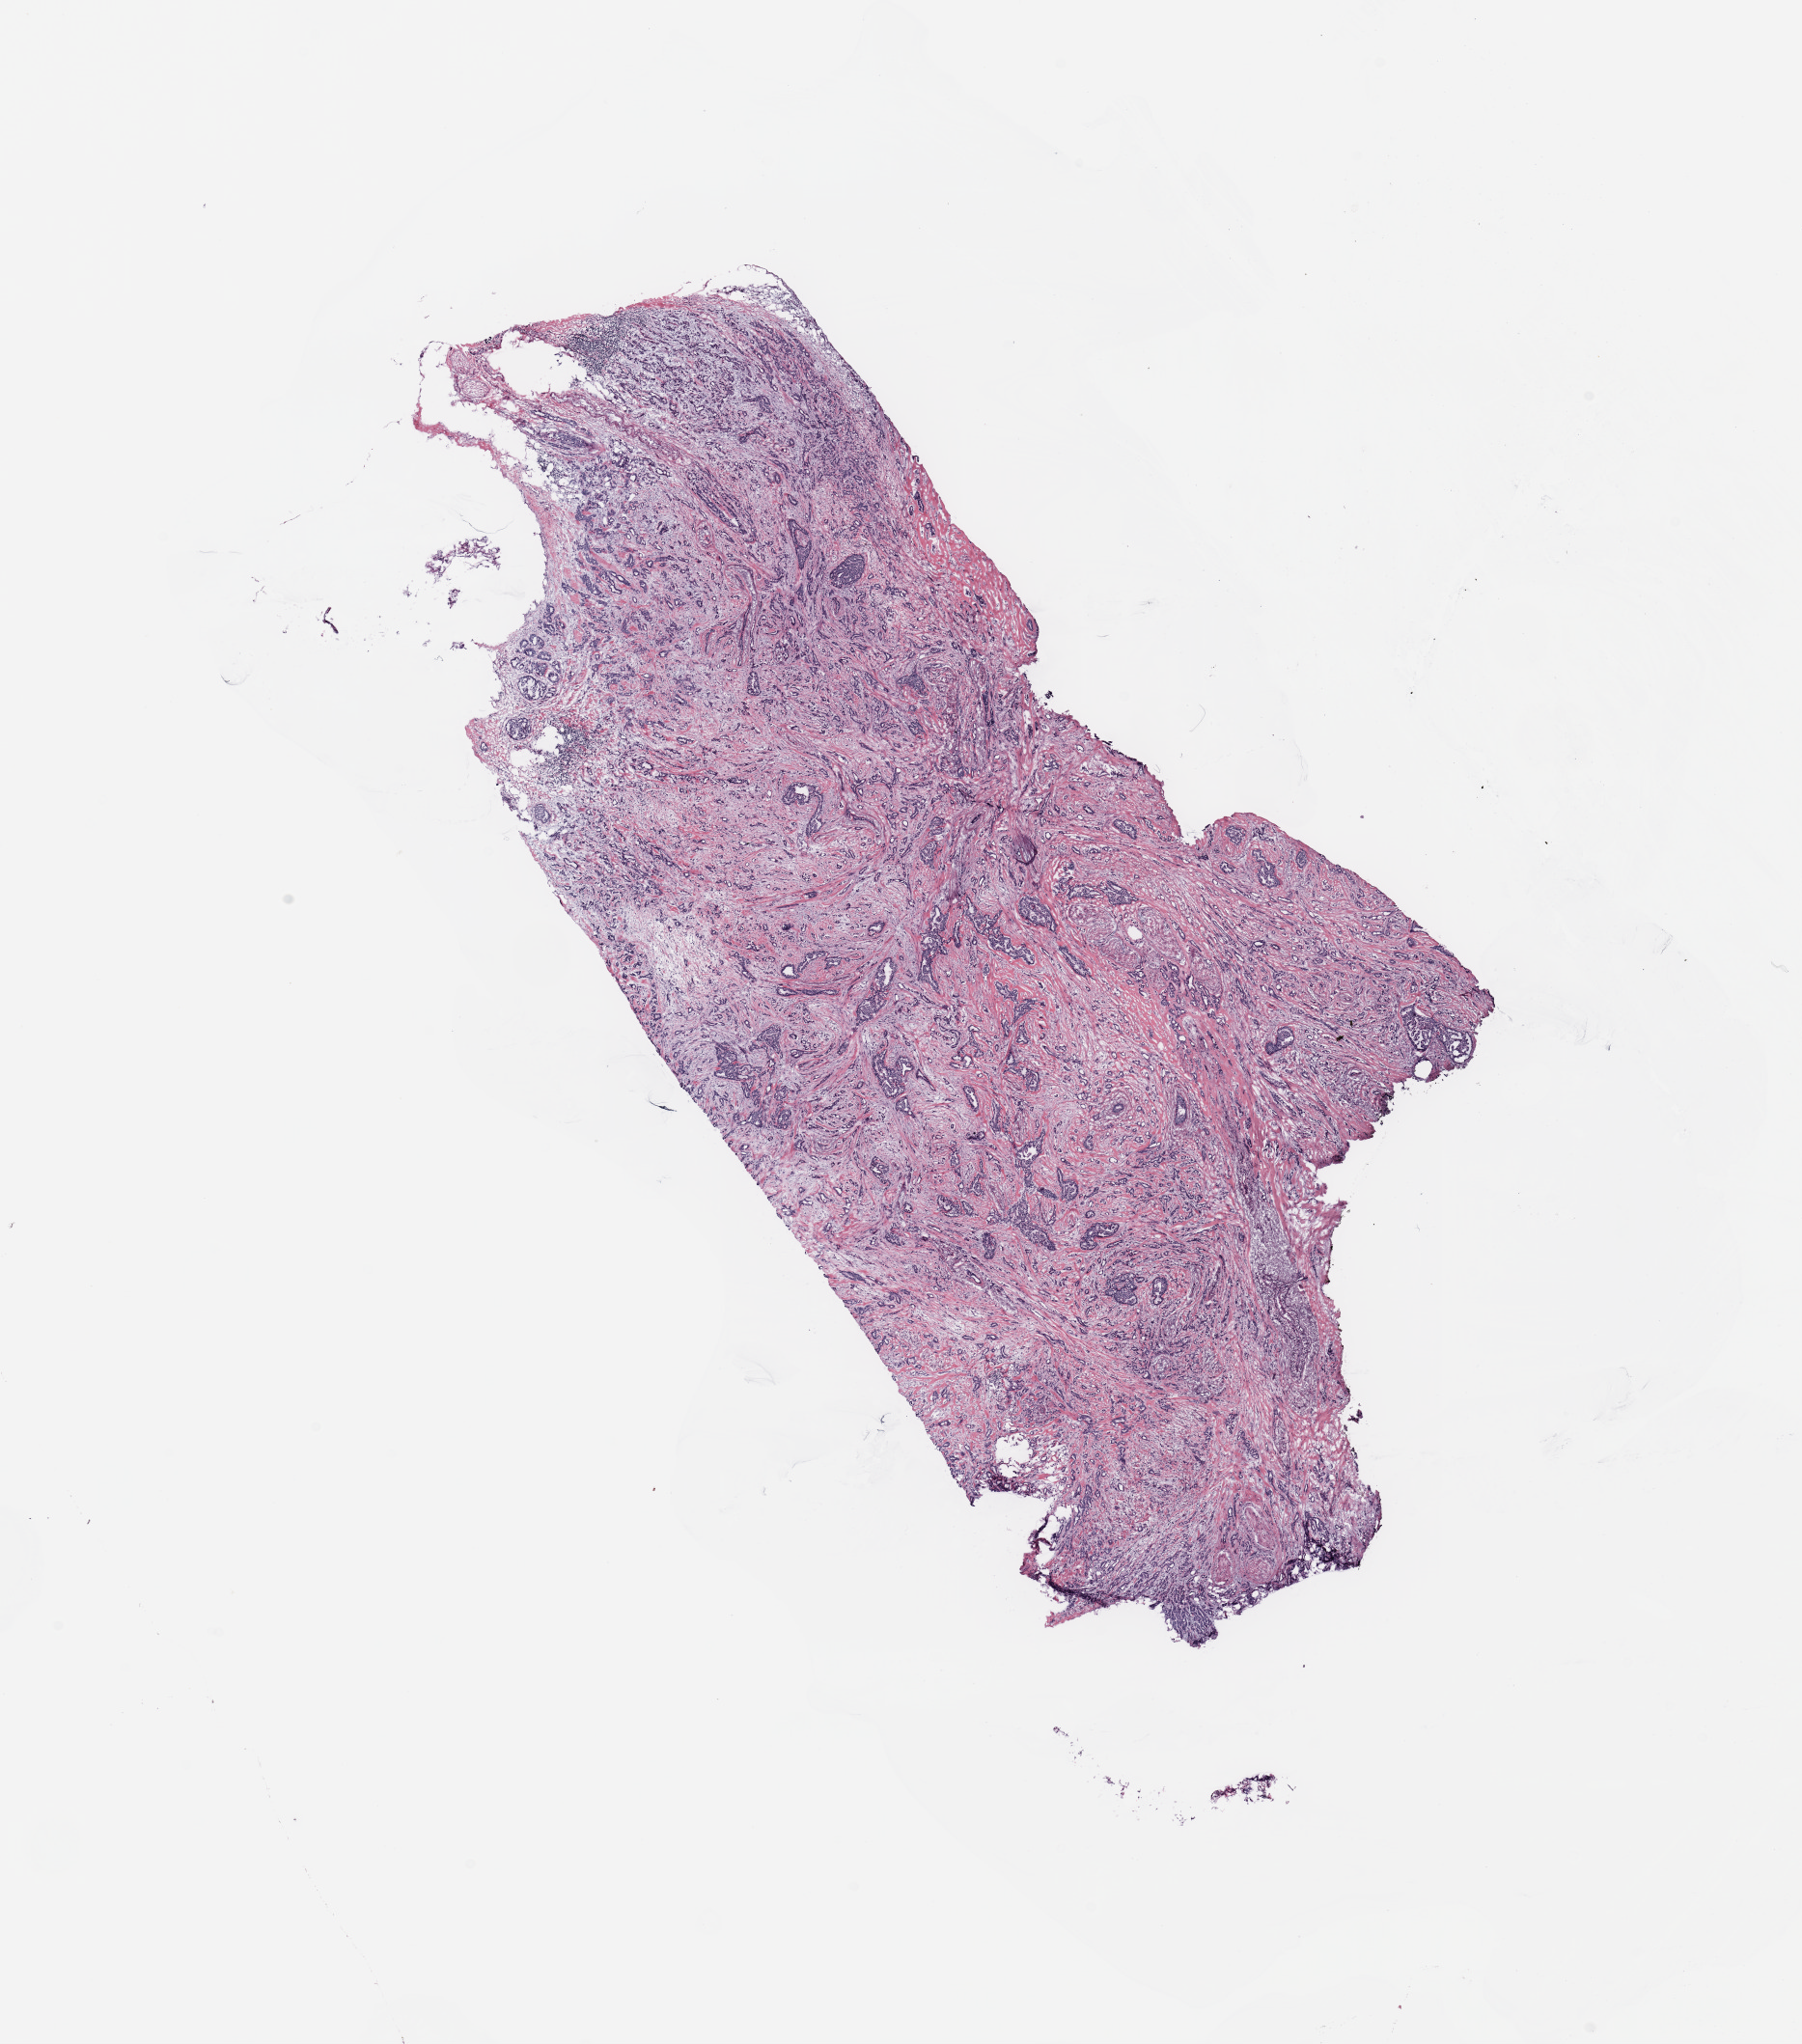
Digitized H&E tissue section (whole slide) — a low-resolution overview of the entire scanned area, about 14.8 x 16.8 mm. Breast, tissue type not recorded.
Patient diagnosis (cohort enrolment): breast cancer (breast).